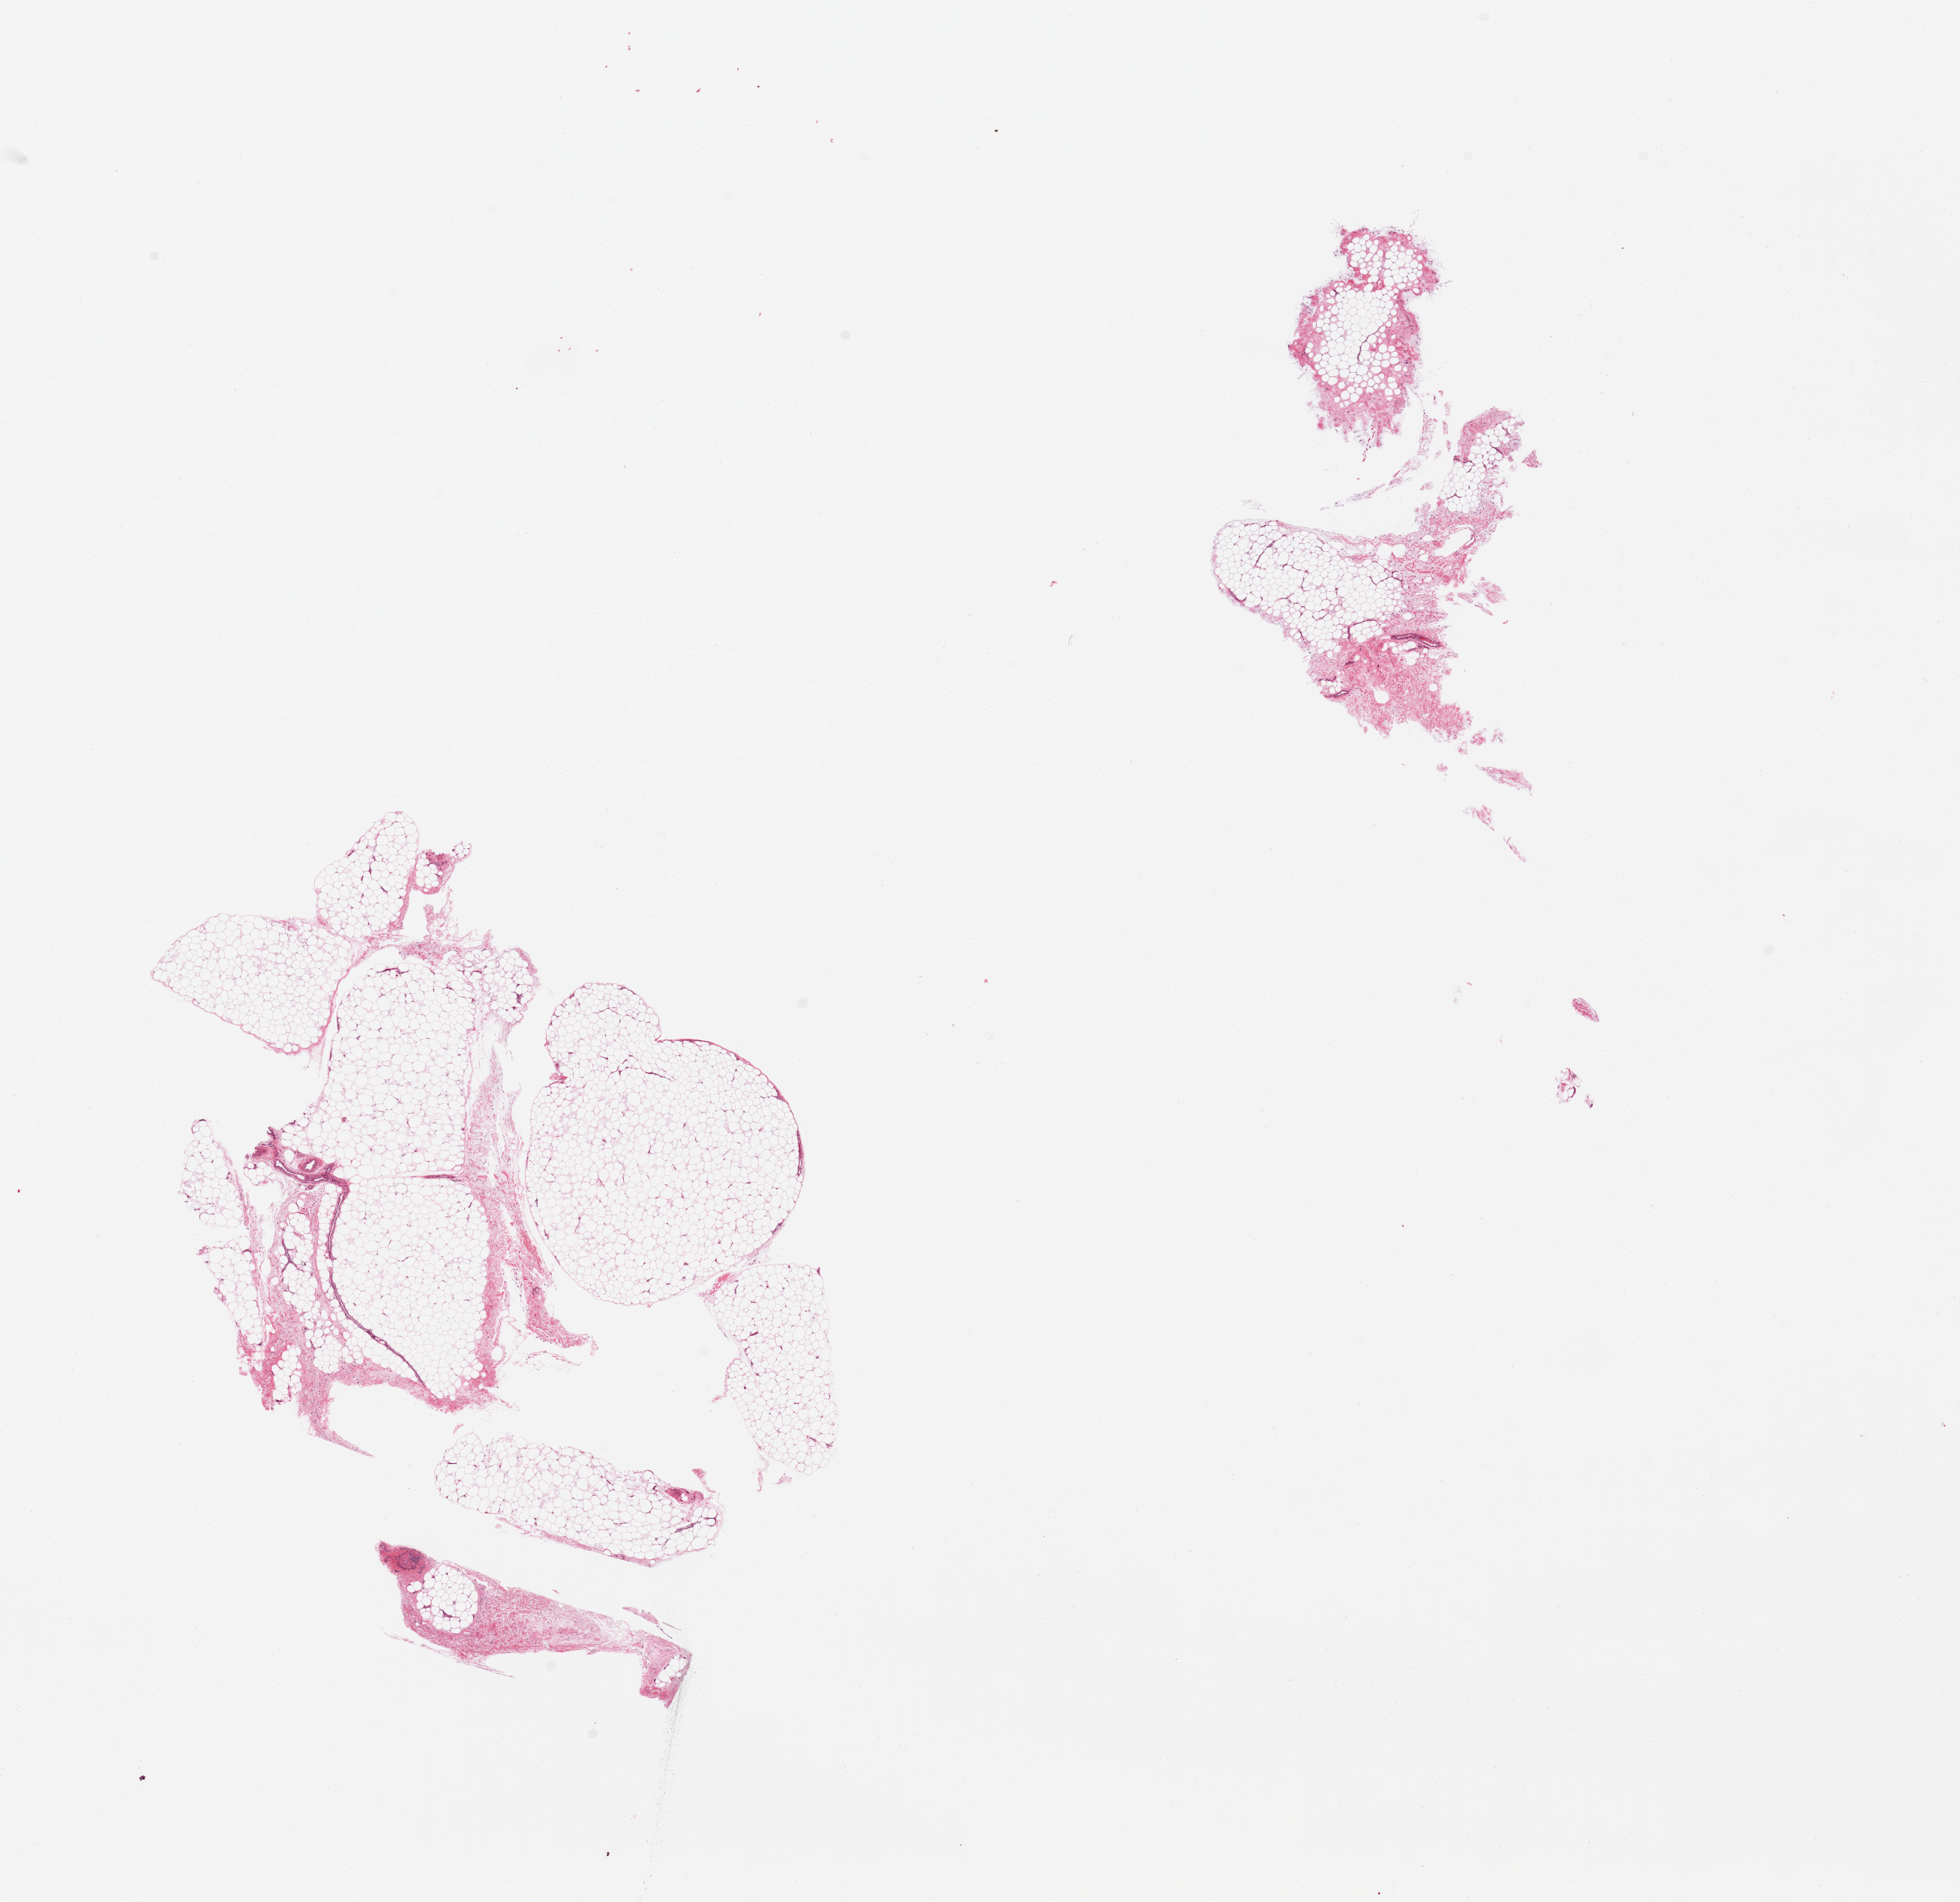
Whole-slide image, haematoxylin and eosin stain — a low-resolution overview of the entire scanned area, about 20.7 x 20.1 mm (acquisition: 20x scan), PAXgene-fixed paraffin-embedded (PFPE) section, section of adipose tissue (target tissue), tissue donor sample. Male donor.
Reviewer comment on this tissue sample: 2 pieces.